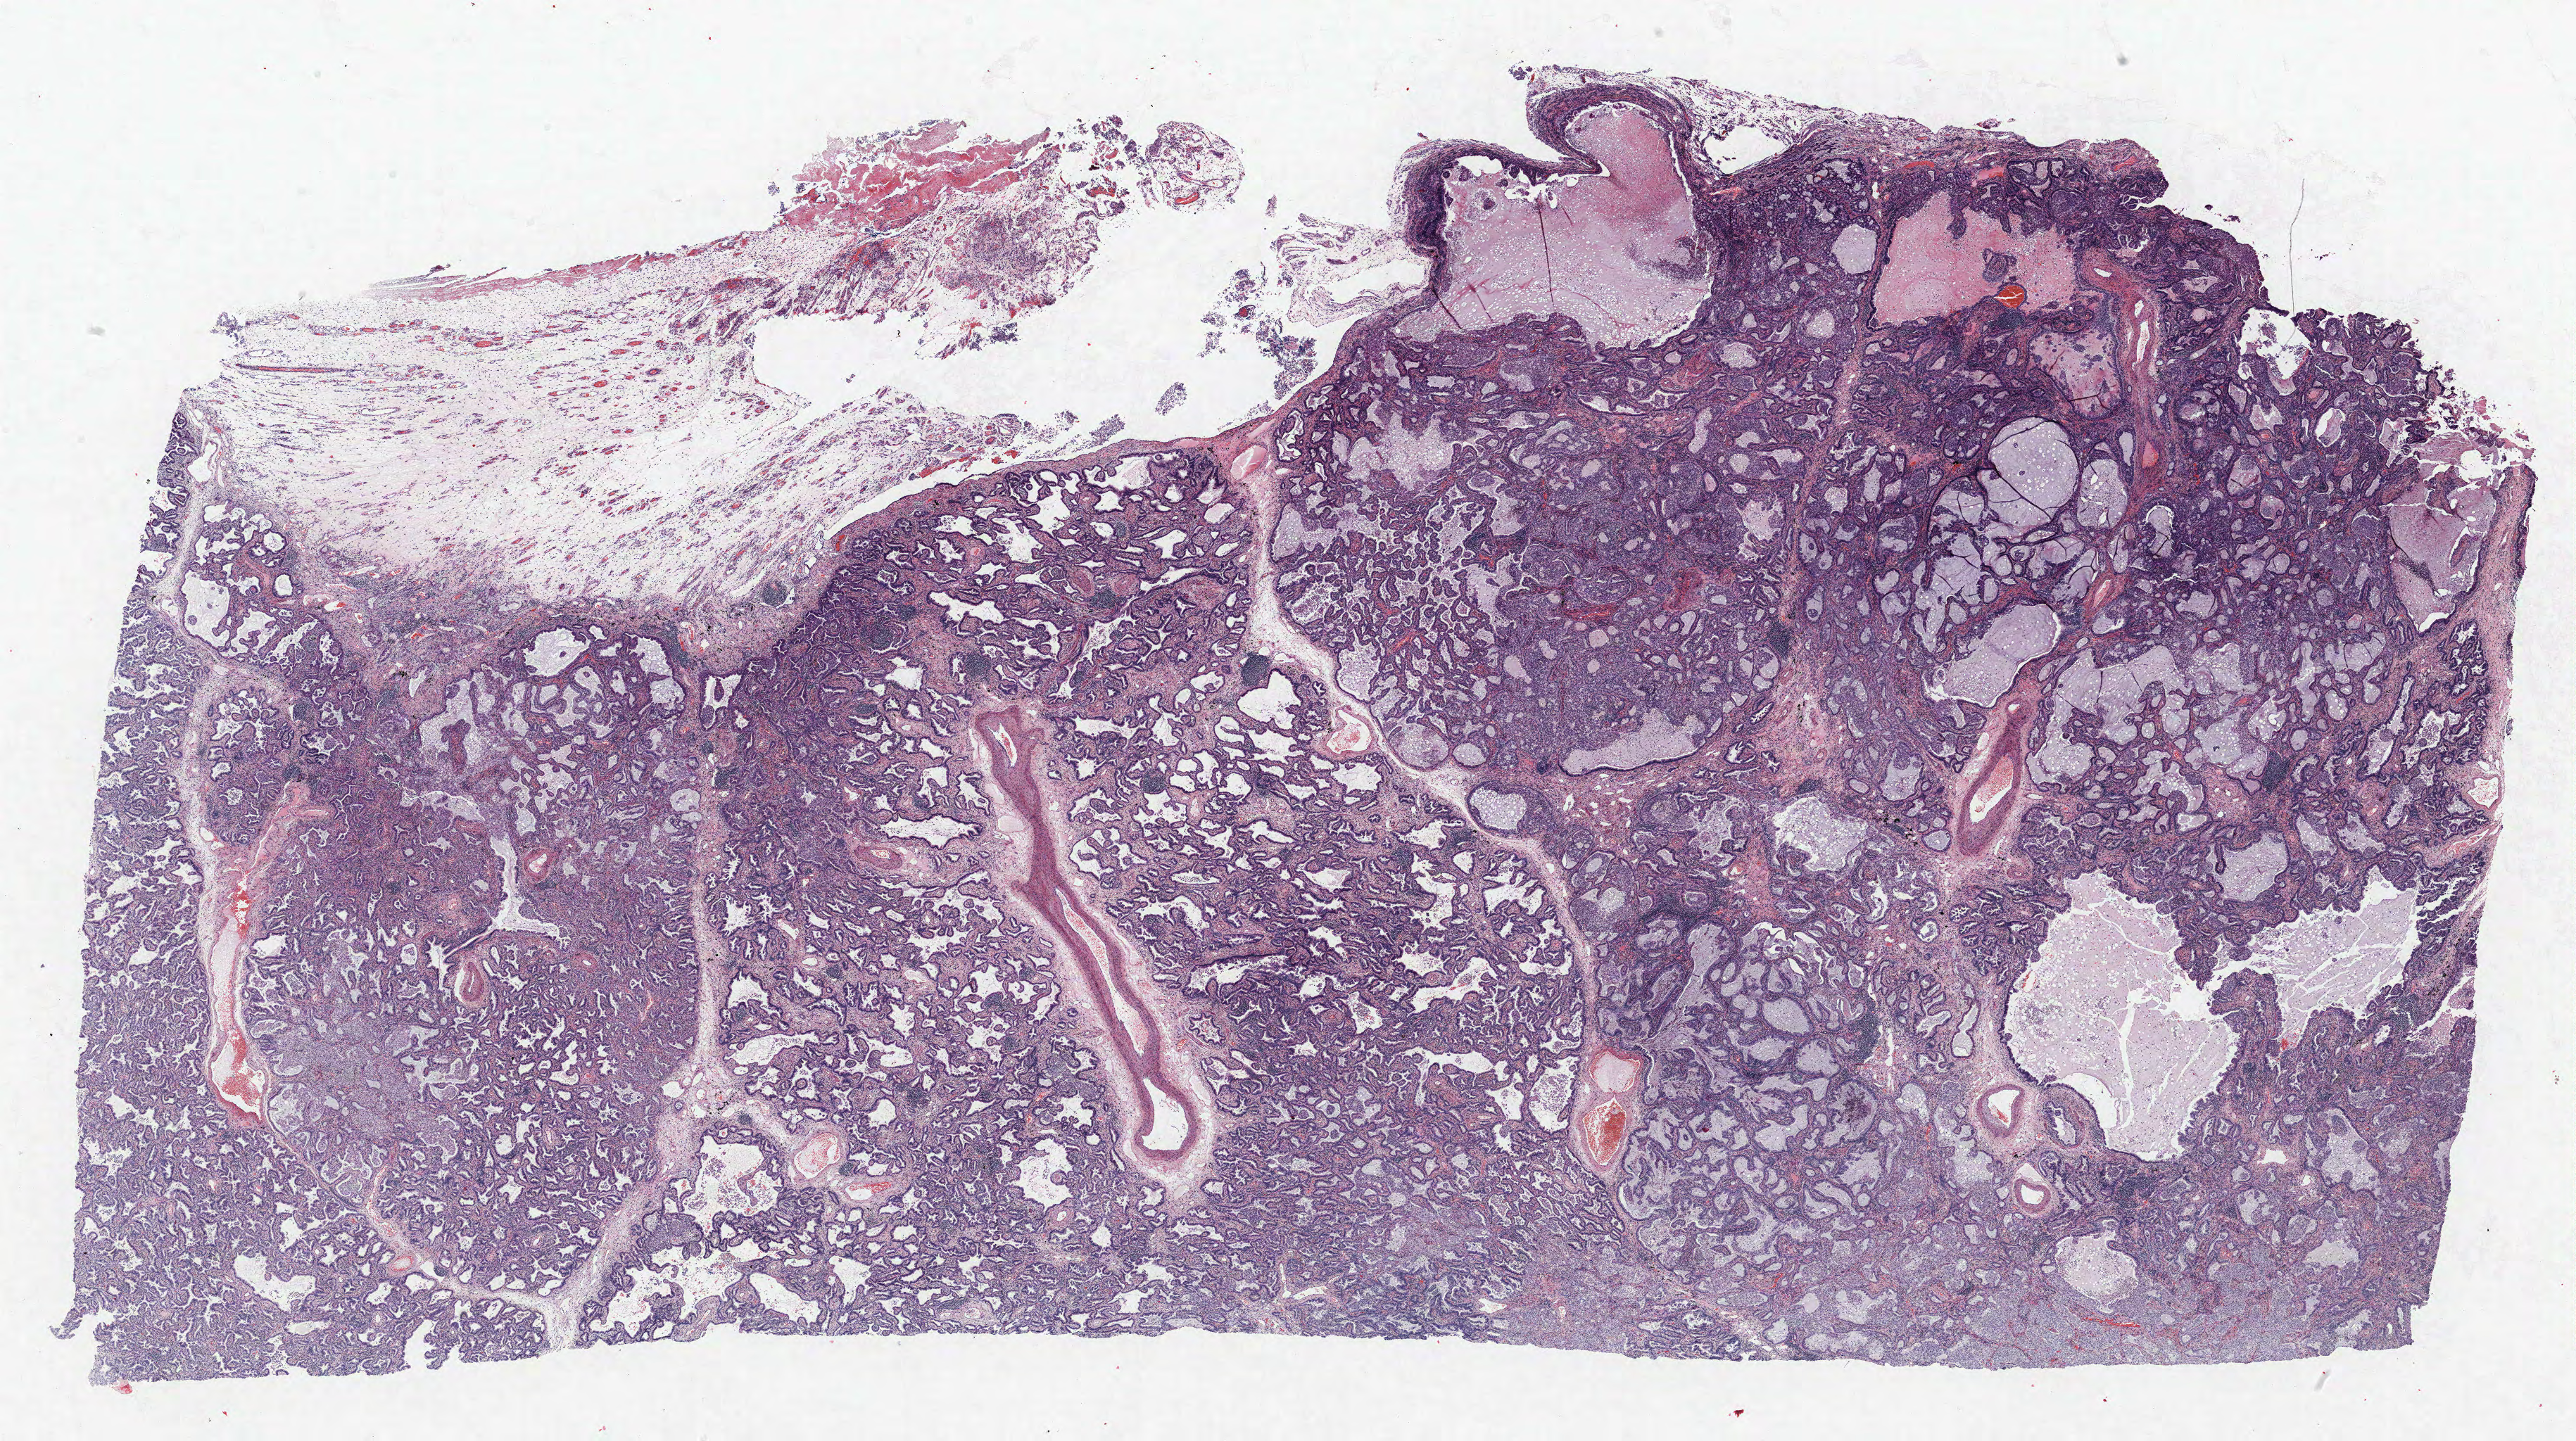
H&E-stained whole-slide image, low-resolution overview of the scanned area, about 29.3 x 16.4 mm; formalin-fixed paraffin-embedded (FFPE) section; lung. Female, age 73 at enrolment. Former smoker at enrolment.
Participant's lung-cancer diagnosis: Mucinous adenocarcinoma (ICD-O-3 8480/3).